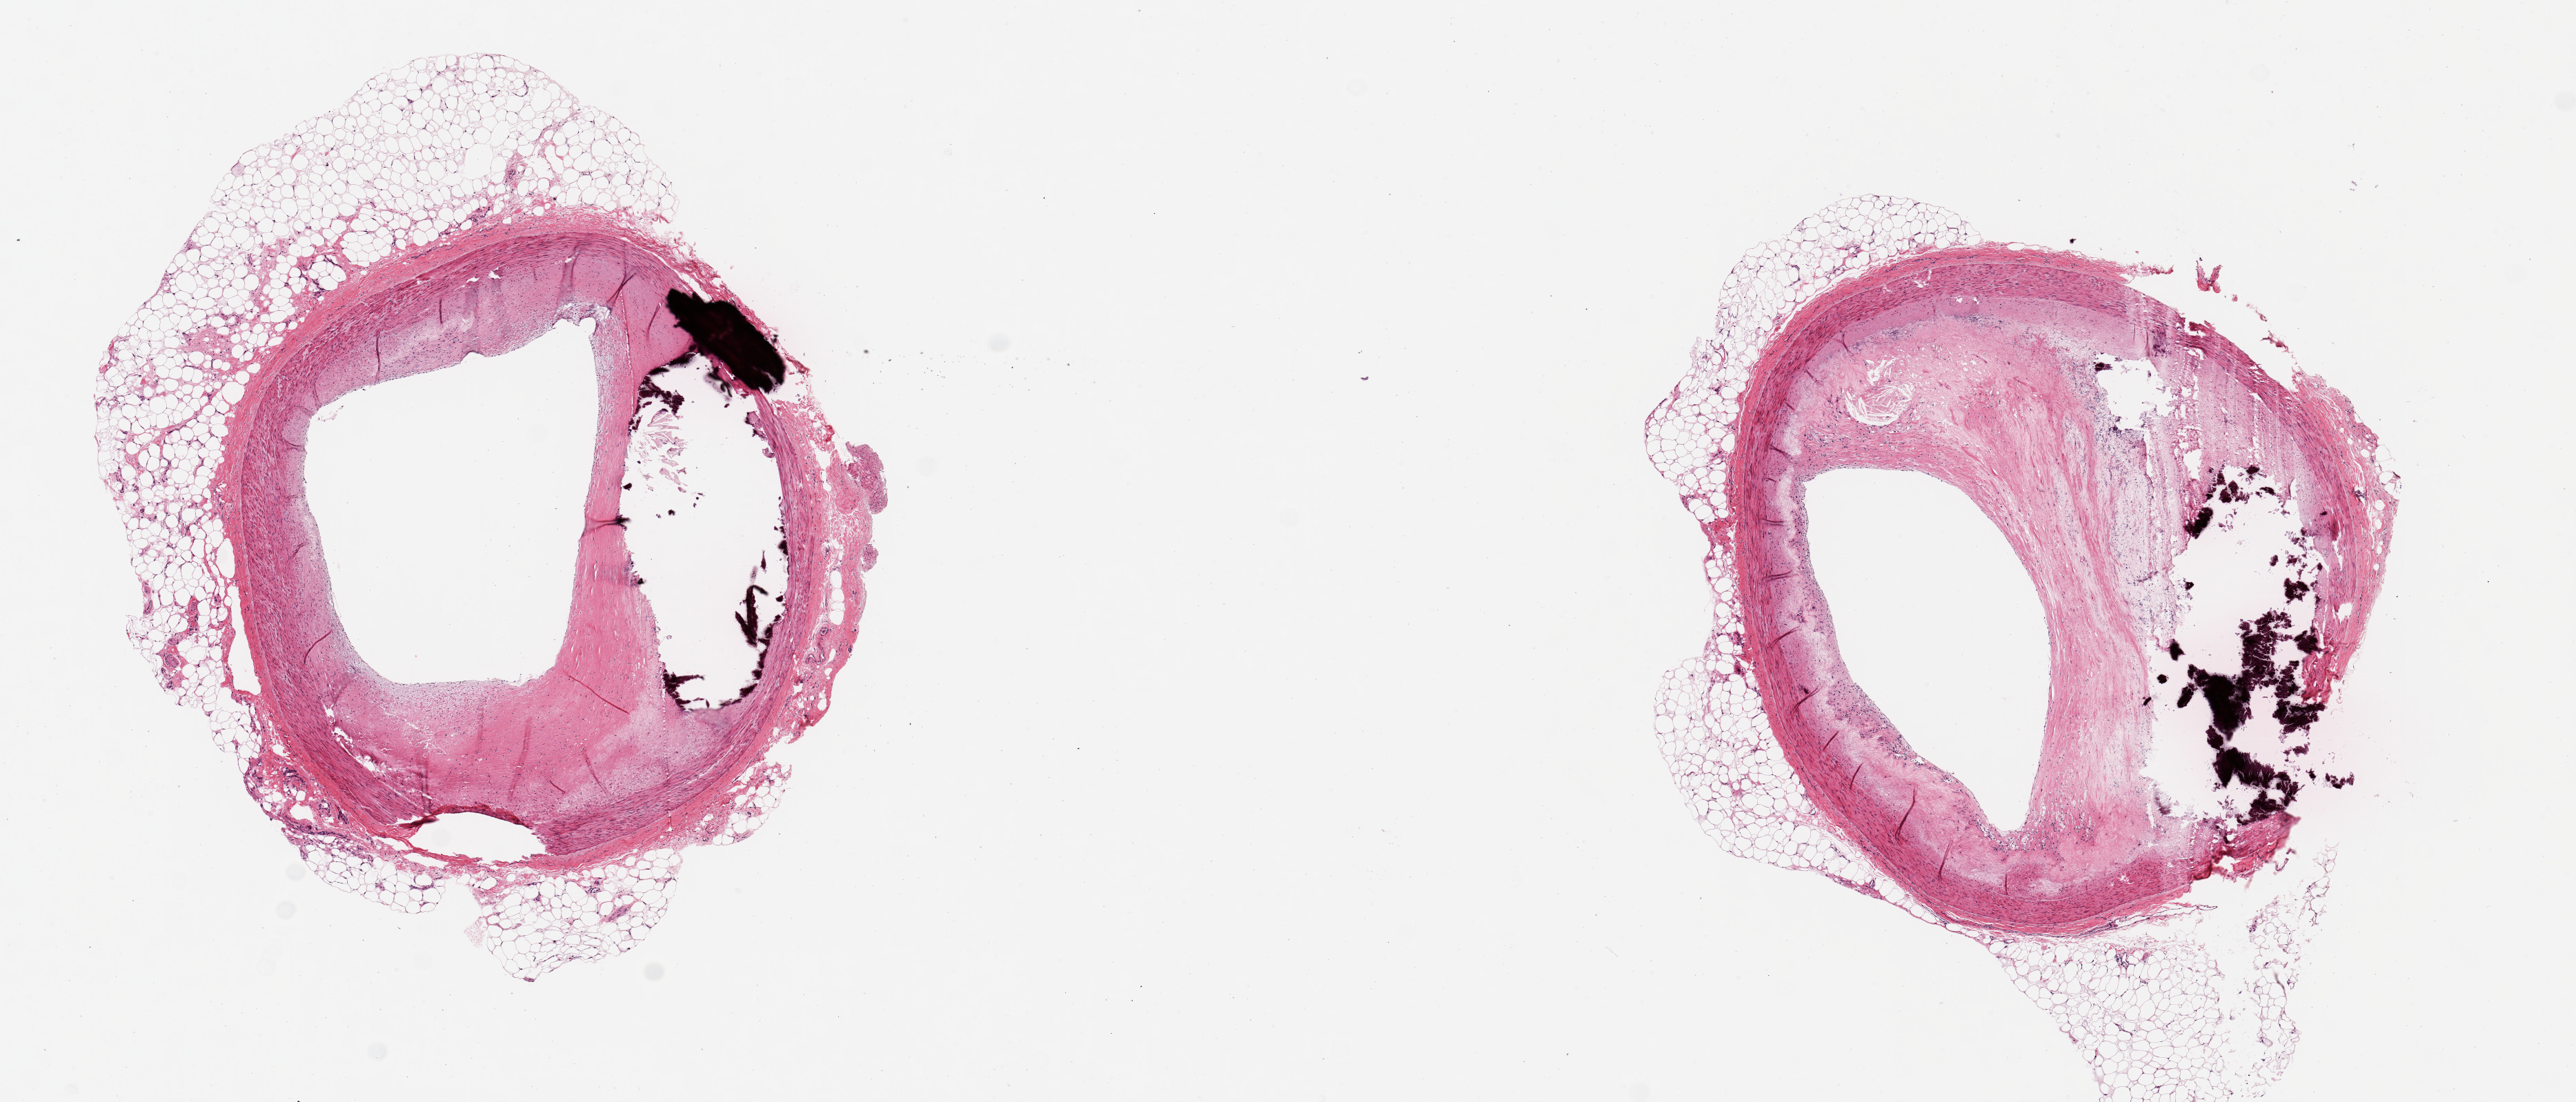
H&E whole-slide image, a low-resolution overview of the entire scanned area, about 14.8 x 6.3 mm (from a 20x scan), PAXgene-fixed, paraffin-embedded tissue, target tissue: coronary artery, tissue donor sample. Donor sex: male.
- review note (as recorded): 2 ~3.5mm d. pieces ~60% occlusive atherosclerosis